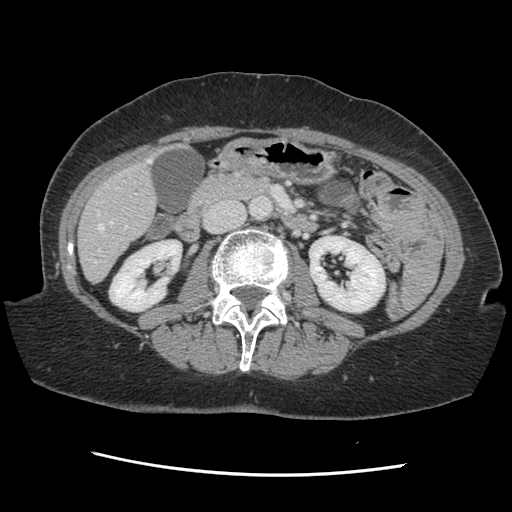
Contrast-enhanced abdominal CT, one axial slice. Slice 51 of 141 in the series (ordered by position). 120 kVp. Soft-tissue window (W 400 / L 40 HU). 2.5 mm slice thickness. 512 × 512 image matrix, field of view 330 × 330 mm. Female patient, age 61 years. From the clinical record (not read from this slice): diagnosis: colorectal cancer liver metastases, imaged before liver resection; multiple liver metastases: no; largest metastasis: 2.4 cm; disease in both lobes: no.
Structures marked on this image (outlined manually by an expert reader):
- hepatic veins: bounding box [x1, y1, x2, y2] px = [95, 159, 152, 263]
- liver: [79, 156, 157, 281]
- planned liver remnant (the part of the liver to remain after resection): [79, 192, 156, 281]
- portal vein (with intrahepatic branches): [98, 226, 127, 251]